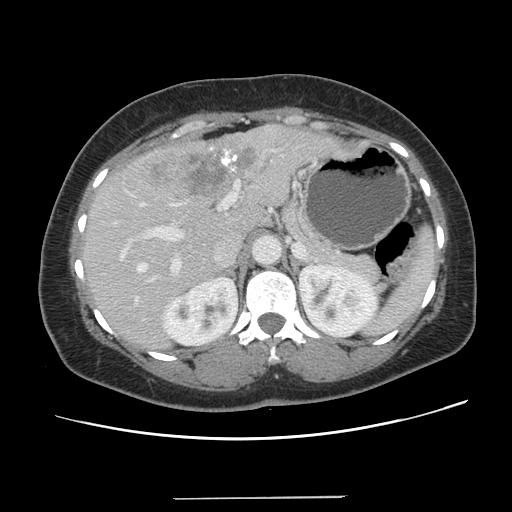
Contrast-enhanced abdominal CT, one axial slice; position 85 of 141 along the scan axis; intravenous contrast given; soft-tissue window (W 400 / L 40 HU); 512 × 512 image matrix, field of view 366 × 366 mm. Female patient, age 53 years. Case-level facts recorded for this patient, not image findings: diagnosis: colorectal cancer liver metastases, imaged before liver resection; multiple liver metastases: no; largest metastasis: 14.5 cm; disease in both lobes: yes.
Annotated regions visible in this slice (outlined manually by an expert reader):
- hepatic veins: bounding box <135,202,178,301> (left, top, right, bottom; pixels)
- liver: <82,126,359,350>
- planned liver remnant (the part of the liver to remain after resection): <84,207,264,350>
- portal vein (with intrahepatic branches): <120,180,239,283>
- liver metastasis: <143,146,263,197>